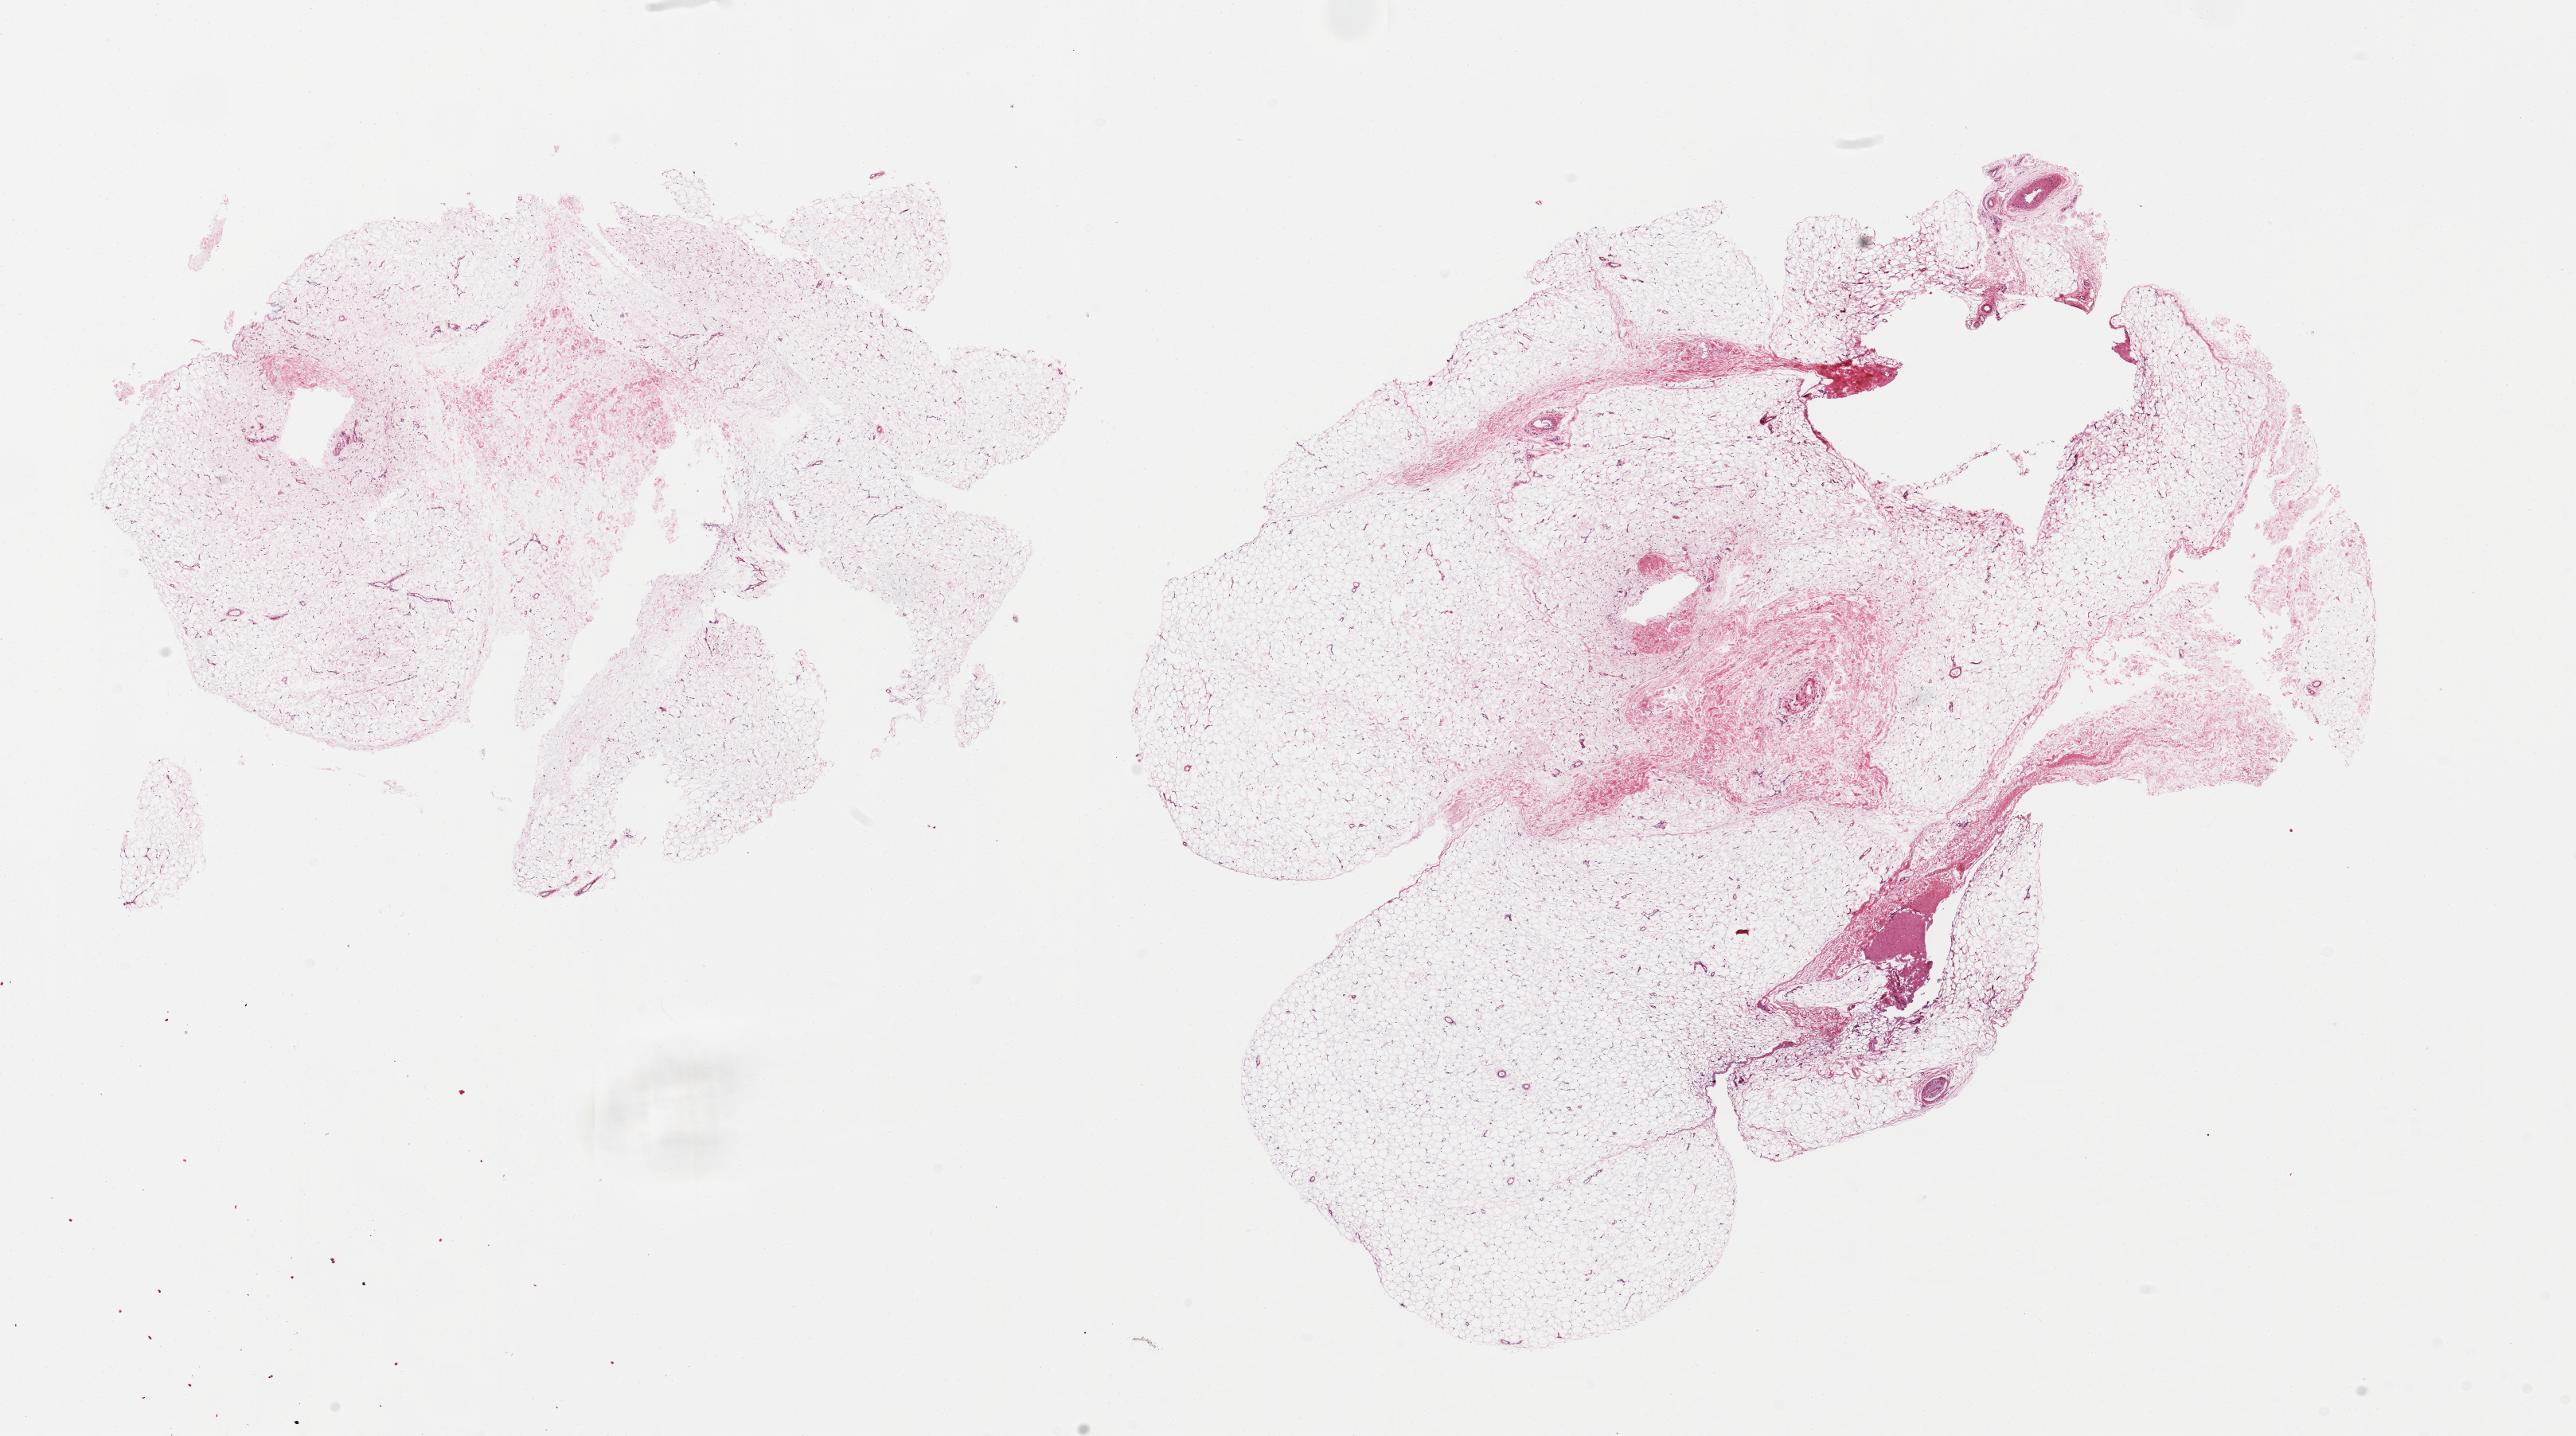
Whole-slide image, hematoxylin and eosin (H&E) stain — whole scanned area (about 25.6 x 14.3 mm) shown as a low-resolution overview, PAXgene-fixed paraffin-embedded (PFPE) section, section of adipose tissue (target tissue), donor tissue sample. Donor: male.
Review note (as recorded): 2 pieces; fascia is ~5% tissue.